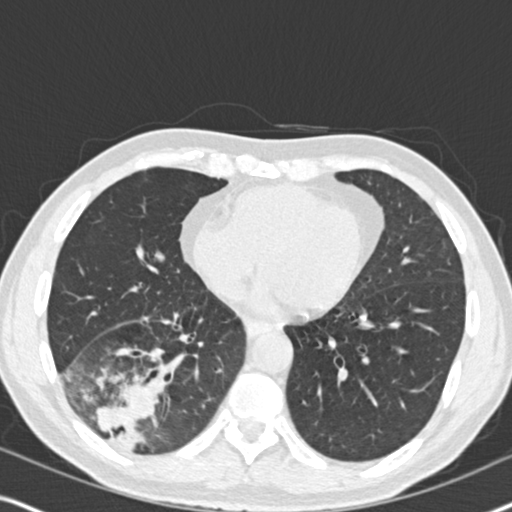
Low-dose screening chest CT, axial slice. Second annual screen. Lung window (W 1500 / L -600 HU). Standard (soft-tissue) reconstruction kernel (B30f). Male participant, aged 61 years at enrolment.
Expert reader's lesion annotation, box from (x=53, y=330) to (x=190, y=465) px. Screening reader's record for this exam (one nodule recorded; not confirmed to be the boxed lesion): non-calcified nodule or mass ≥4 mm, right lower lobe, 90 × 80 mm, soft tissue attenuation, pre-existing on the prior screen: yes; interval growth: yes. Later outcome: lung cancer diagnosed 20 days after this screen — bronchiolo-alveolar adenocarcinoma, NOS, right lower lobe, moderately differentiated (G2), stage IIIB (AJCC 6th edition), 90 mm at pathology.